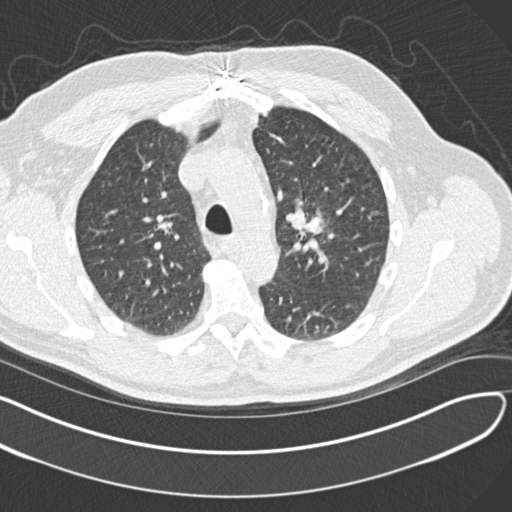
Chest CT (low-dose screening protocol), one axial image. Second screening round (one year after baseline). Lung window (W 1500 / L -600 HU). 2 mm slice thickness. Slice 44 of 164 in the series. 512 × 512 image matrix. Male, age 65 years at enrolment. Former smoker at enrolment.
Expert-annotated lung lesion, bounding box <285,197,341,258> (left, top, right, bottom; pixels). The screening reader recorded 4 non-calcified nodules or masses ≥4 mm on this exam; which of them this box marks is not recorded. Later outcome: lung cancer diagnosed 577 days after this screen (after the third annual screen) — acinar cell carcinoma, left upper lobe, stage IA (AJCC 6th edition), 25 mm at pathology.